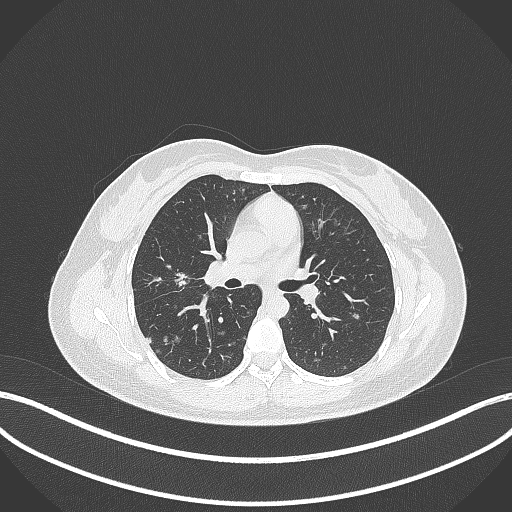
Chest CT, one axial slice; position 194 of 307 along the scan axis; reconstruction kernel B70f; 120 kVp; lung window (W 1500 / L -600 HU); 512 × 512 image matrix. Patient: female, 33 years. Case-level facts recorded for this patient, not image findings: clinical TNM (as recorded): T1c N0 M0.
Outlined on this slice (rectangle marked by the reading radiologist):
- lung tumour (recorded histology: adenocarcinoma): box from (x=173, y=270) to (x=191, y=290) px